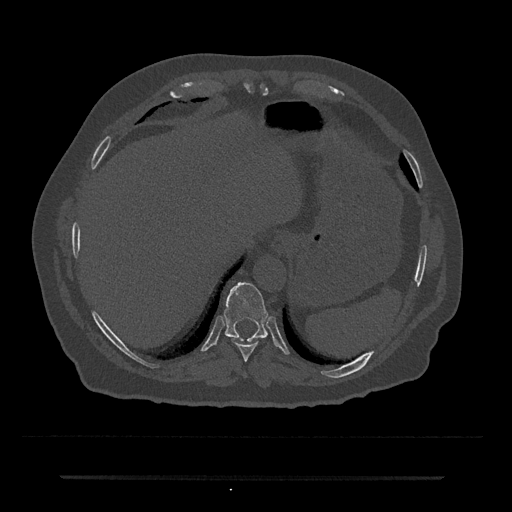
CT including the spine, one axial slice; slice 250 of 797 in the series (ordered by position); bone window (W 1800 / L 400 HU); 0.5 mm slice thickness; 512 × 512 image matrix, field of view 437 × 437 mm. Male patient, age 69 years. Case-level facts recorded for this patient, not image findings: primary cancer: prostate.
Outlined on this slice (semi-automatically segmented with operator editing):
- T10 vertebra: bounding box (x1, y1, x2, y2) in pixels: (223, 282, 268, 342)
- T9 vertebra: (232, 339, 258, 362)